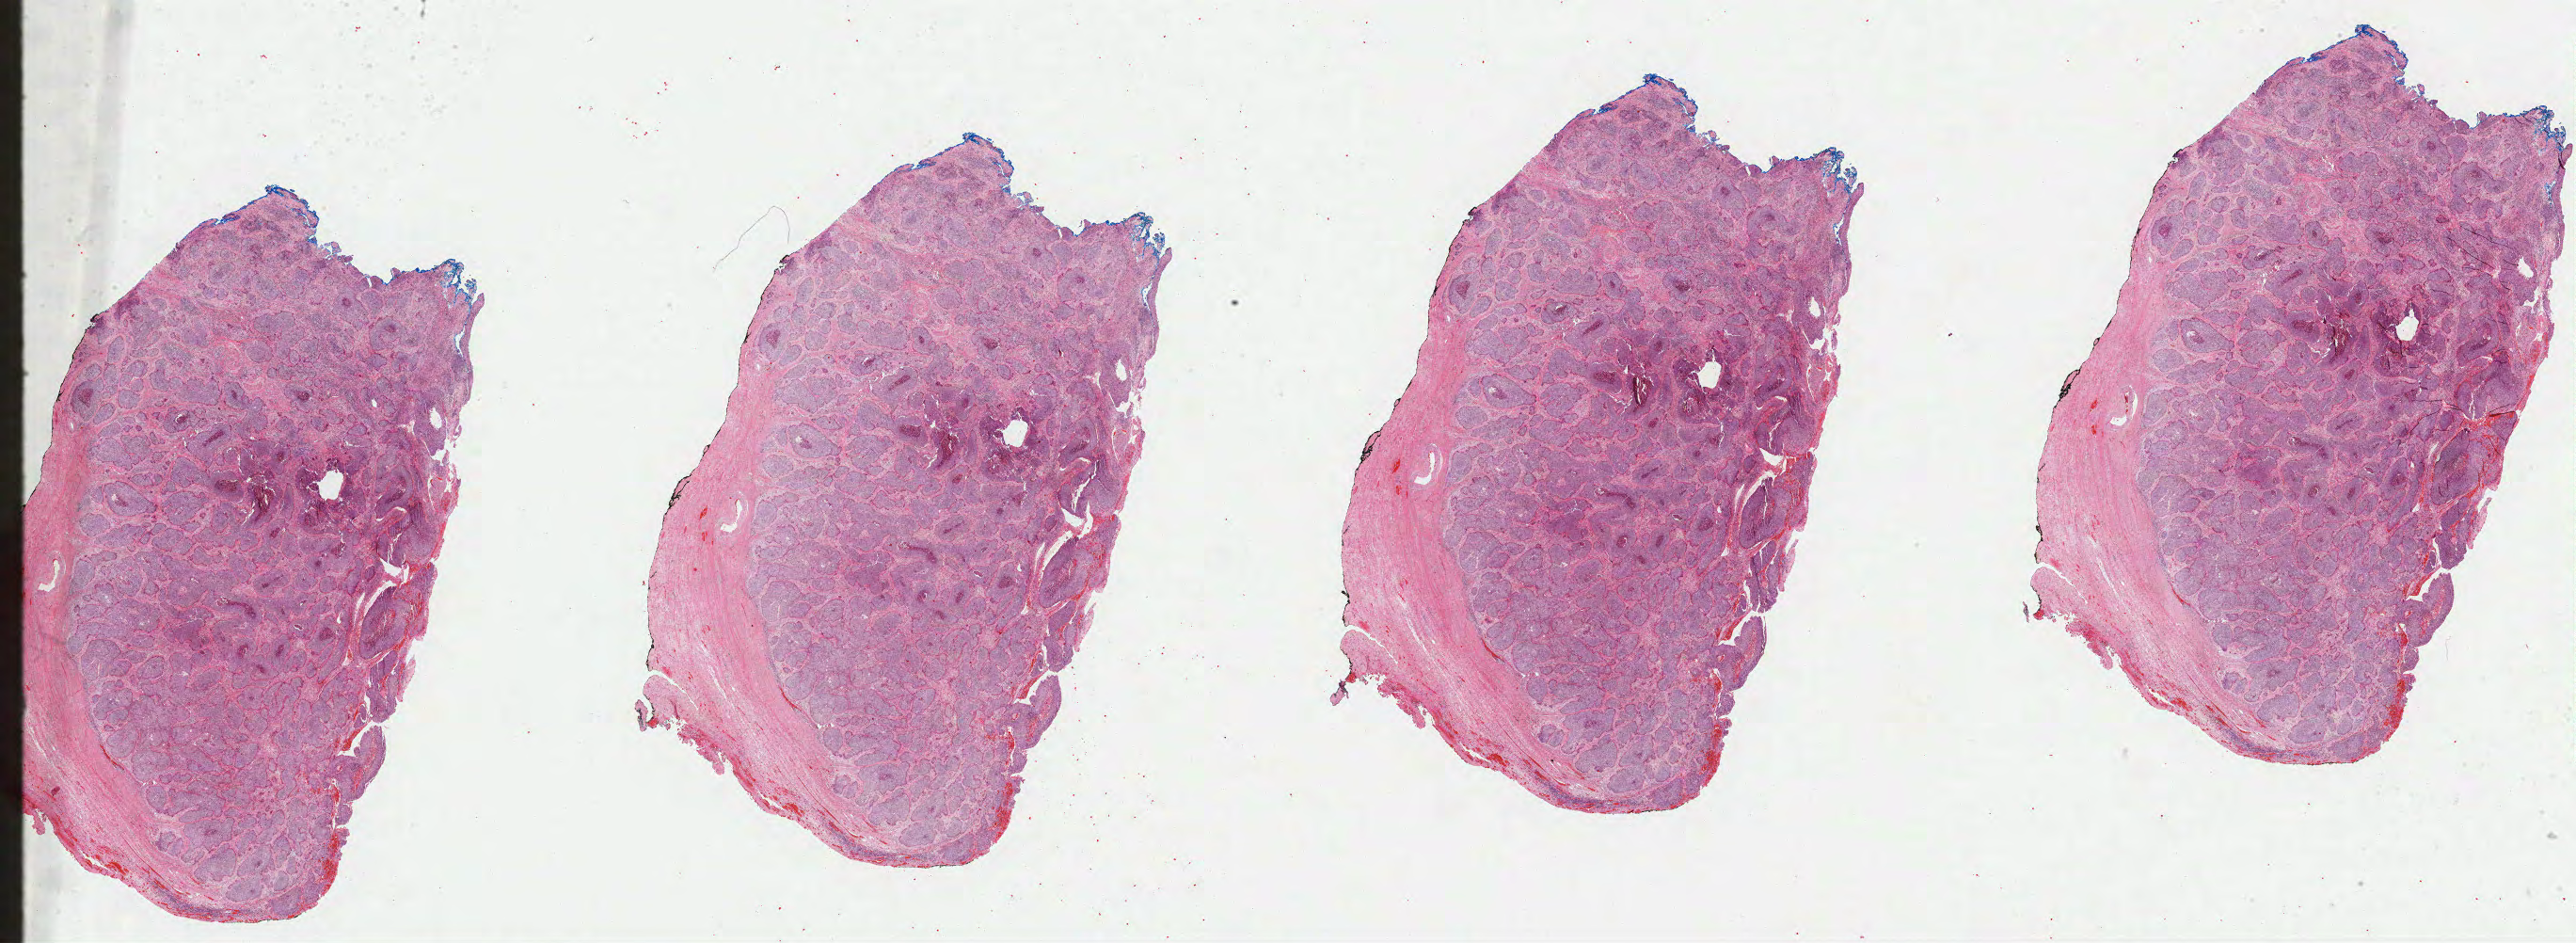
Digitized H&E tissue section (whole slide), shown as a low-resolution overview of the whole scanned area (about 44.1 x 16.1 mm). Formalin-fixed paraffin-embedded (FFPE) diagnostic section. Primary tumour sample from the cervix. Female patient; age at initial diagnosis 64 years. Histologic grade: G2 (moderately differentiated).
Histologic diagnosis: Squamous cell carcinoma, large cell, nonkeratinizing, NOS. FIGO stage: IB1.